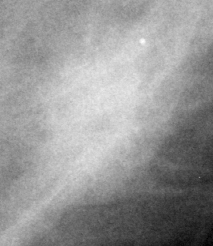
Crop from a digitized film mammogram around one marked abnormality; left breast; CC view.
- Mass, shape irregular, margins spiculated; BI-RADS assessment category 4; pathology (as recorded): malignant.